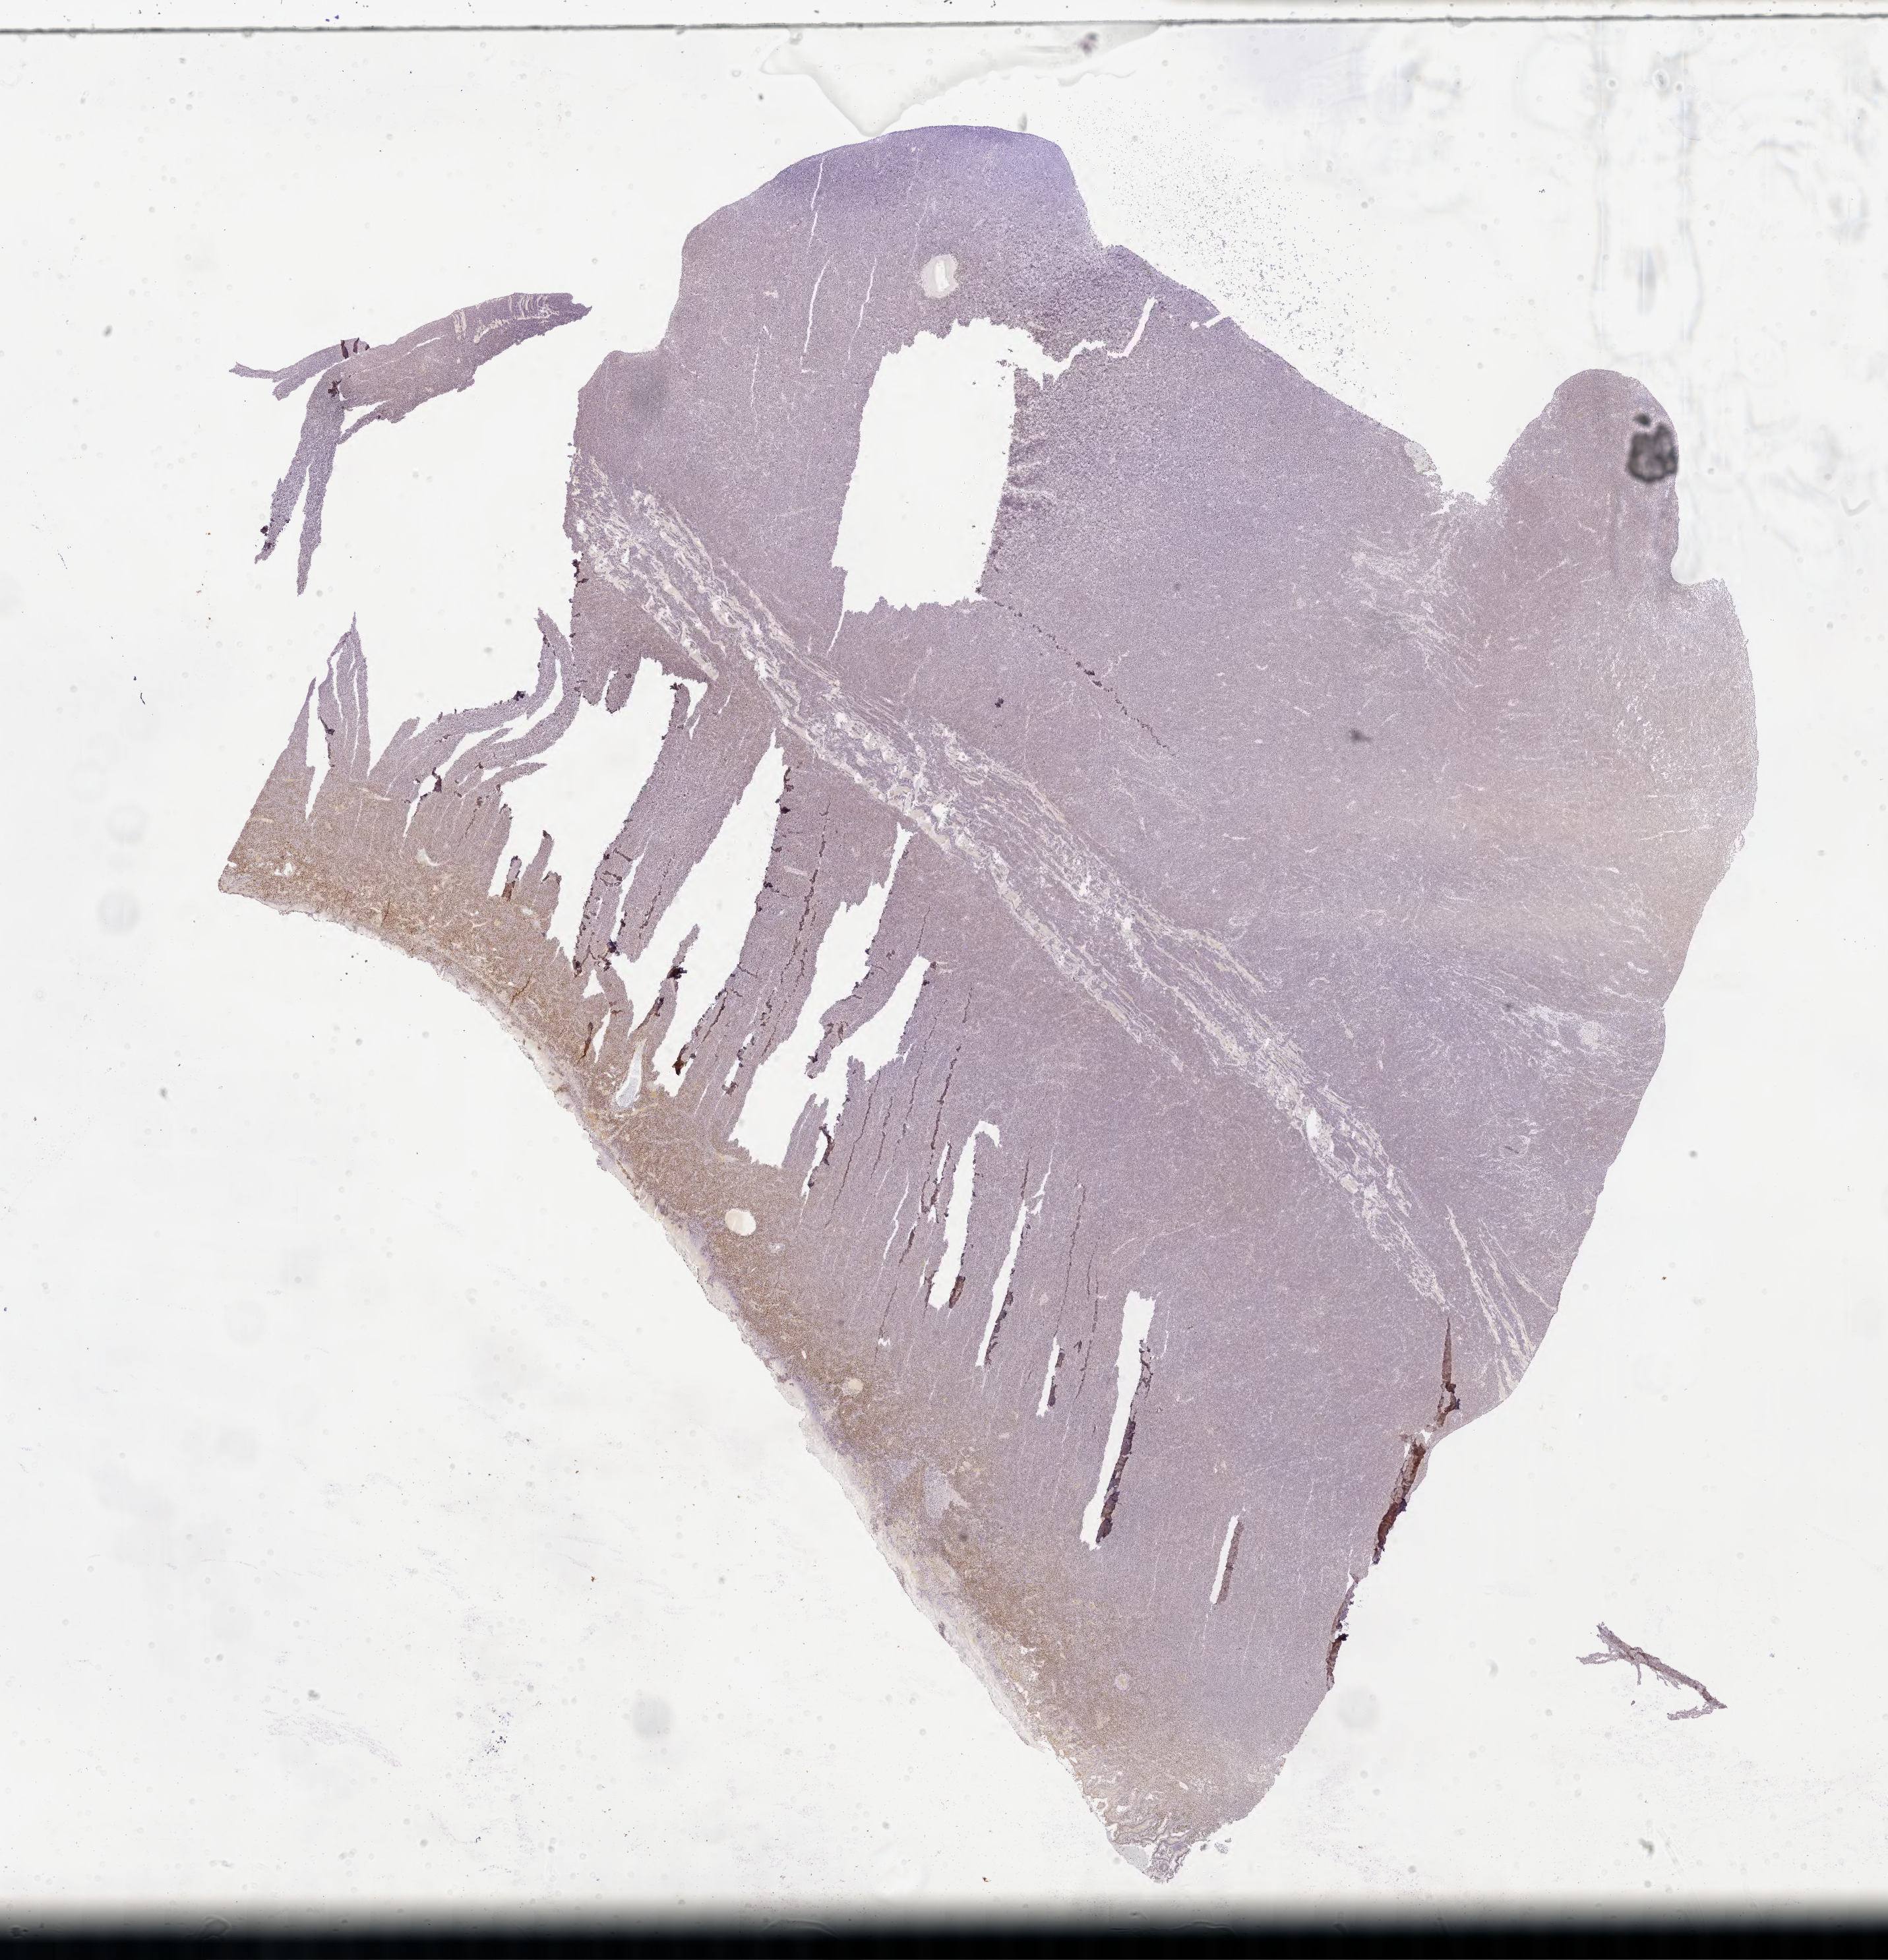
Whole-slide image, immunohistochemical stain for BCL6 — a low-resolution overview of the entire scanned area, about 23.1 x 24.0 mm. Tumor tissue. Patient male; age 36 years.
Histologic diagnosis: Burkitt lymphoma, NOS.